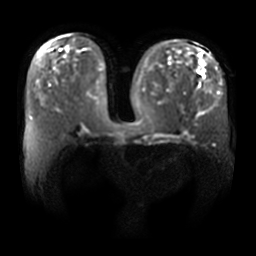
Breast MRI, one axial slice; position 16 of 36 along the scan axis; diffusion-weighted series; image 2 of 4 stored at this slice position (different b-values; order by instance number); 3 T; 5 mm slice thickness; 256 × 256 image matrix, field of view 400 × 400 mm. Female patient.
Annotated regions visible in this slice (outlined manually by an expert reader):
- tumour on diffusion-weighted imaging: box from (x=198, y=72) to (x=204, y=78) px